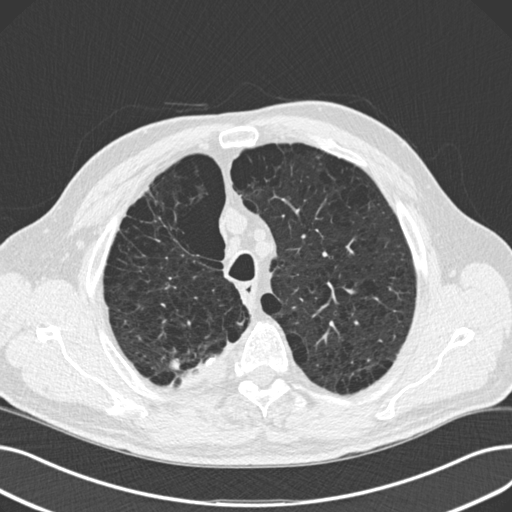
Low-dose screening chest CT, one axial slice; position 123 of 165 along the scan axis; 120 kVp; lung window (W 1500 / L -600 HU); 2 mm slice thickness; 512 × 512 image matrix.
Structures marked on this image (expert manual segmentation):
- lesion 2 (tumor, upper lobe of right lung): bounding box <170,359,180,370> (left, top, right, bottom; pixels)